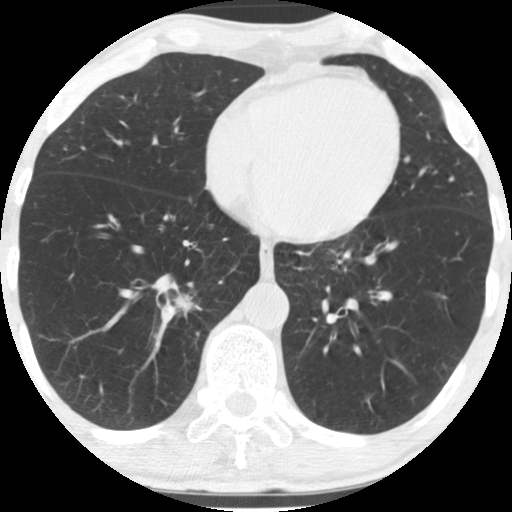
Low-dose screening chest CT, axial slice; first (baseline) screen; lung window (W 1500 / L -600 HU). Male participant, aged 67 years at enrolment.
- Lesion marked by an expert reader, box from (x=156, y=276) to (x=221, y=330) px.
- The exam's reader record, not a measurement of the box and not confirmed to be the same lesion: non-calcified nodule or mass ≥4 mm, right lower lobe, 16 × 16 mm, spiculated (stellate) margins, soft tissue attenuation.
- Lung cancer was diagnosed 49 days after this screen: squamous cell carcinoma, NOS, right lower lobe, moderately differentiated (G2), stage IA (AJCC 6th edition), 20 mm at pathology.